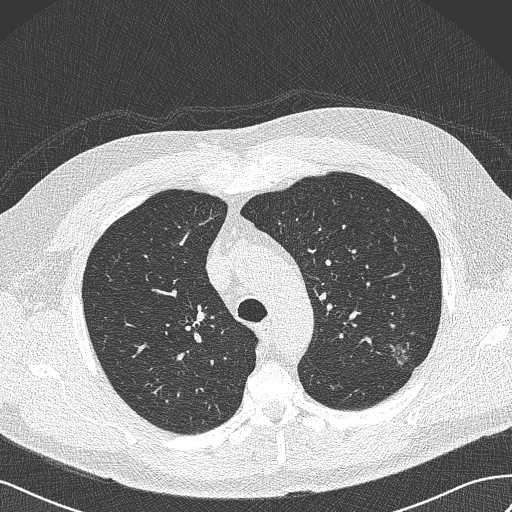
Low-dose screening chest CT, axial slice. First (baseline) screen. Lung window (W 1500 / L -600 HU). Lung (sharp) reconstruction kernel (B50f). 512 × 512 image matrix, field of view 360 × 360 mm. Male participant, aged 65 years at enrolment. Former smoker at enrolment.
Lesion marked by an expert reader, bounding box <383,340,420,371> (left, top, right, bottom; pixels). The screening reader recorded 3 non-calcified nodules or masses ≥4 mm on this exam; which of them this box marks is not recorded. Official screen result: positive, change unspecified: nodule(s) >= 4 mm or enlarging nodule(s), mass(es), or other non-specific abnormalities suspicious for lung cancer. Lung cancer was diagnosed 541 days after this screen (after the second annual screen): adenocarcinoma, NOS, left upper lobe, poorly differentiated (G3), stage IA (AJCC 6th edition), 13 mm at pathology.